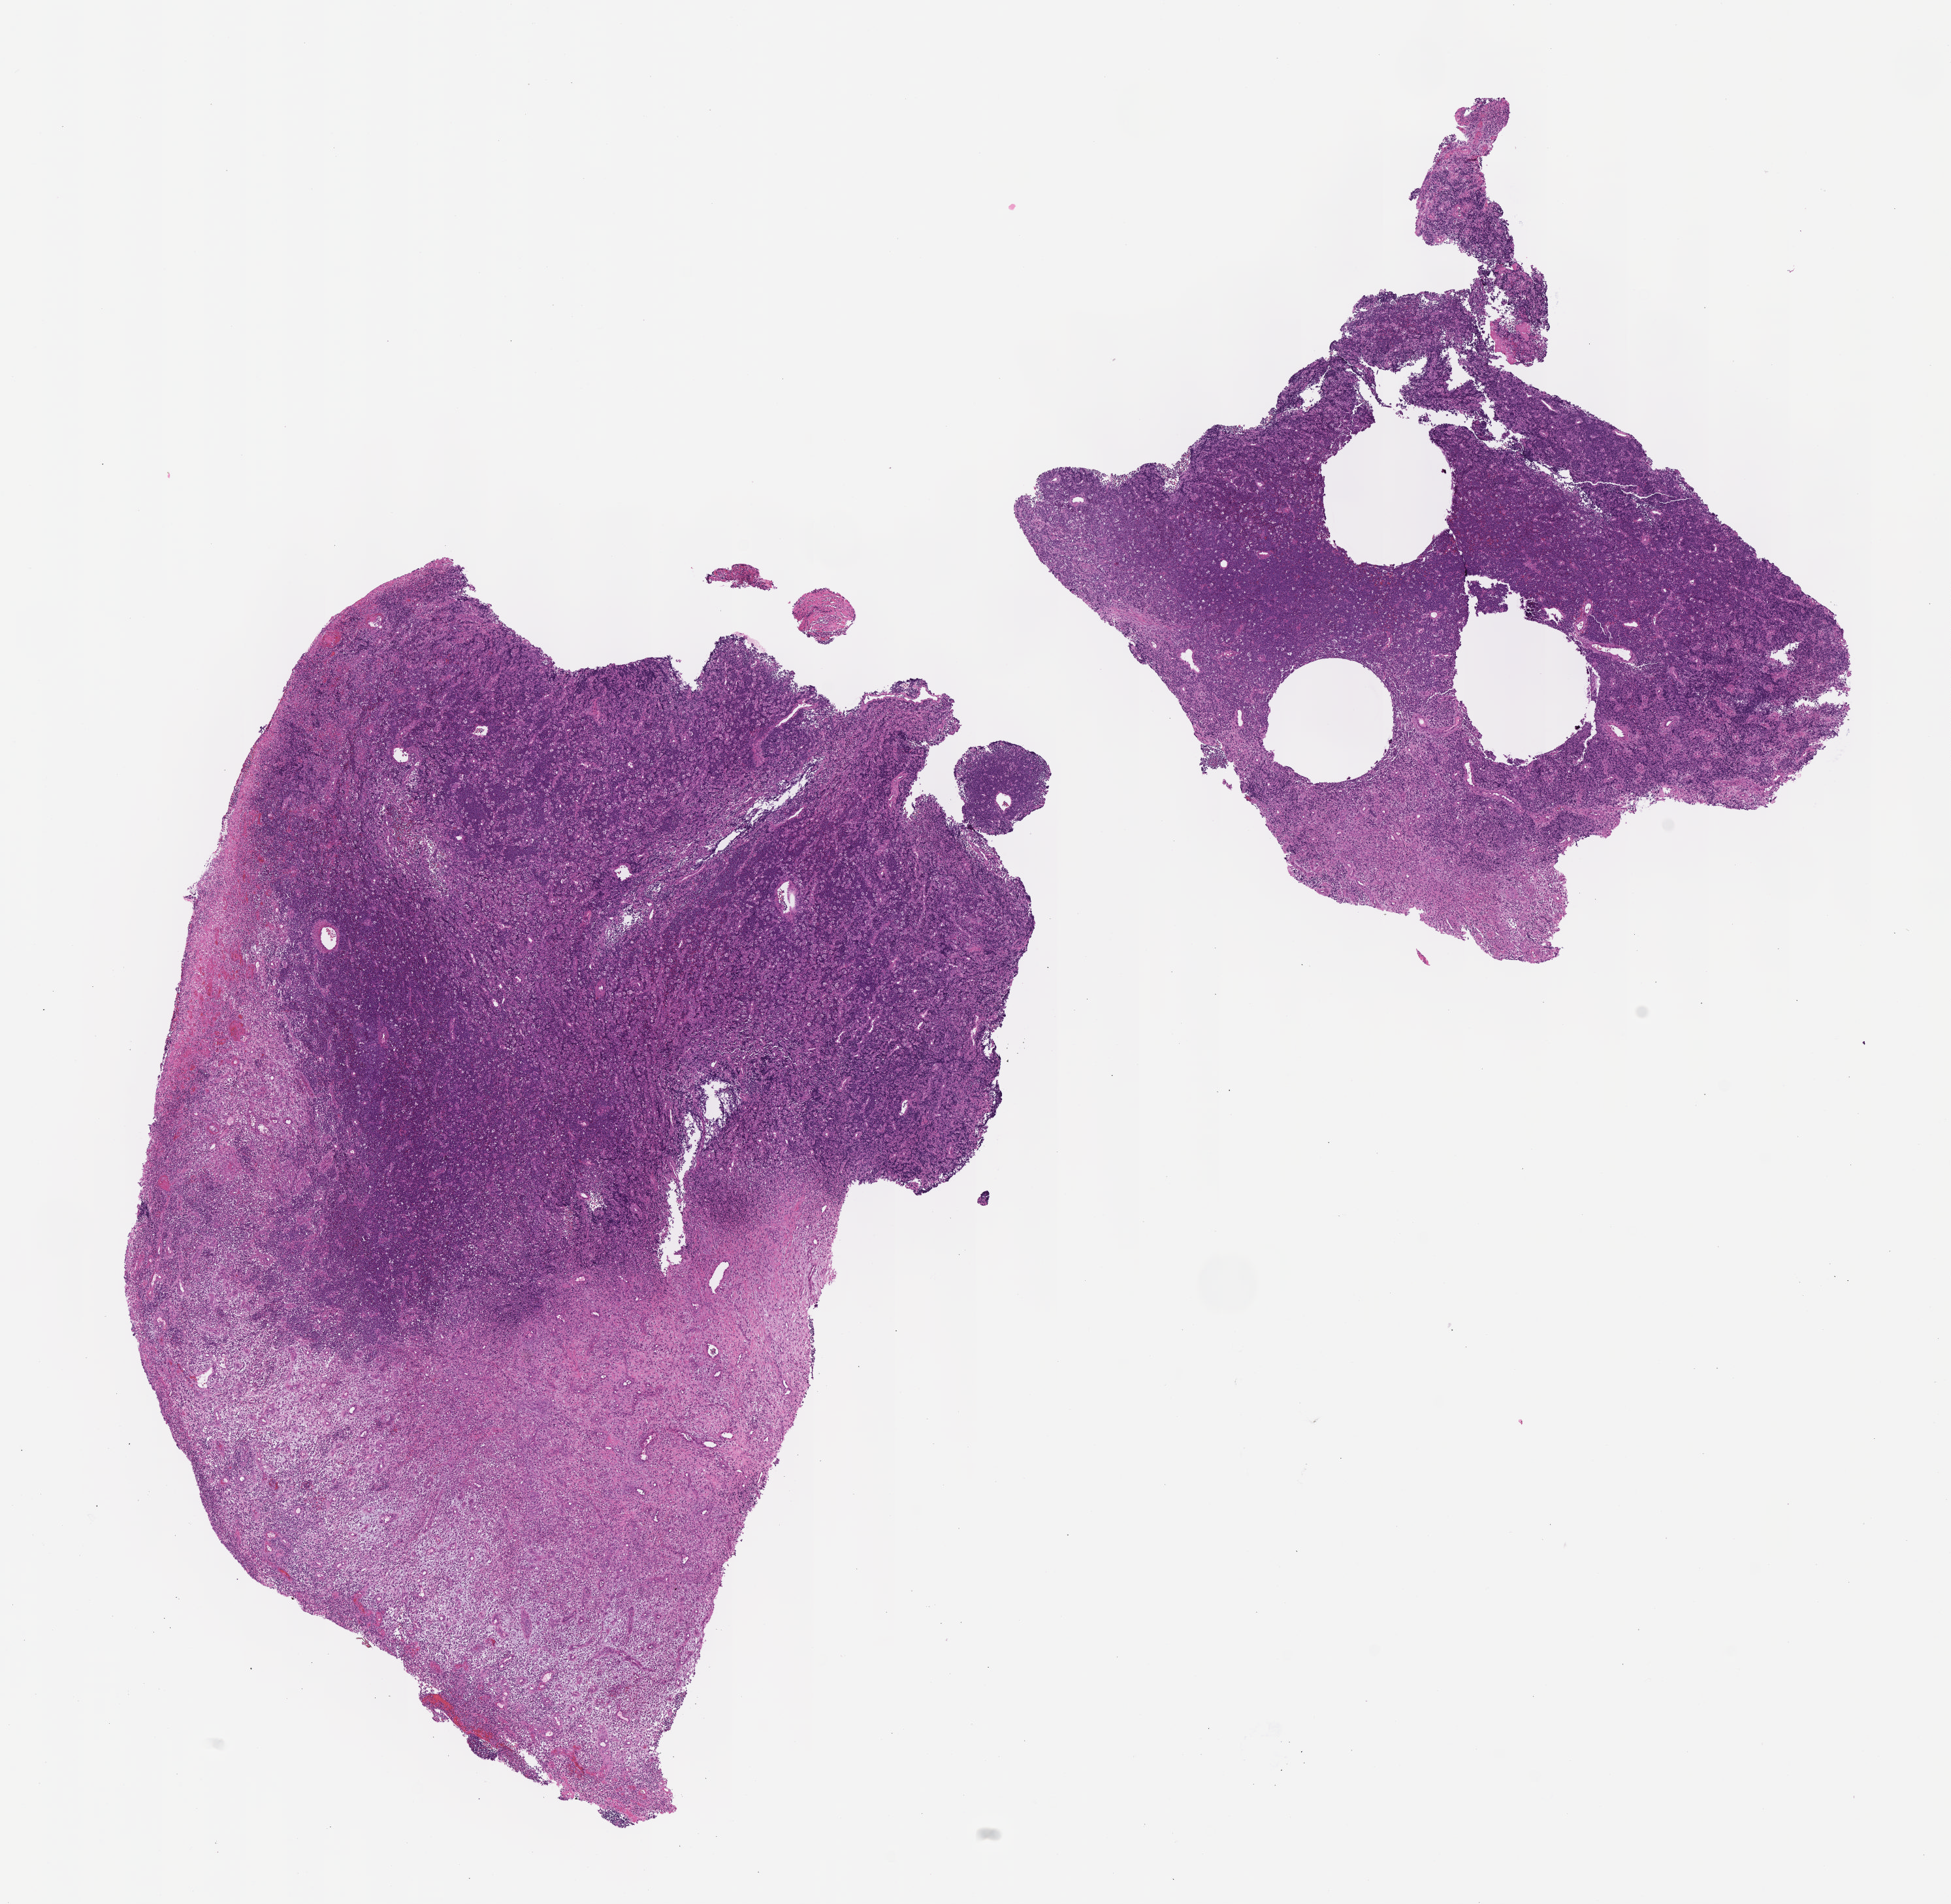
Whole-slide image, H&E stain, whole scanned area (about 12.1 x 11.8 mm) shown as a low-resolution overview. Formalin-fixed, paraffin-embedded (FFPE) tissue. Primary tumor. Anatomic site: cranium. Patient: female, age 11 years. Composition of this section per pathologist review: tumor cells 60%, tumor nuclei 85%, stromal cells 10%, necrosis 20%, normal cells 10%. Inflammatory infiltration, as recorded: lymphocyte infiltration 40%, monocyte infiltration 30%, neutrophil infiltration 20%.
Diagnosis: Burkitt lymphoma, NOS. Section: bottom of the tissue portion. Ann Arbor stage (patient): Stage I.